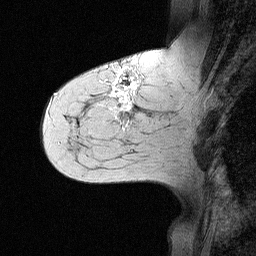
Breast MRI (dynamic contrast-enhanced), one sagittal slice; slice 21 of 64 in the series (ordered by position); dynamic contrast-enhanced study with each time point stored as its own series, time point 2 of 3 at this slice position (early post-contrast, ordered by acquisition time); 1.5 T; TE 4.5 ms, TR 11 ms; 256 × 256 image matrix. Female patient, age 55 years. From the clinical record (not read from this slice): setting: breast cancer imaged before/during neoadjuvant chemotherapy; receptor status: triple-negative.
Structures marked on this image (semi-automatically segmented with operator editing):
- analysis volume of interest (the breast-tissue region the enhancement analysis was run in; not a lesion): bounding box (x1, y1, x2, y2) in pixels: (71, 63, 147, 145)
- tumour enhancement mask (voxels above the 90 % enhancement threshold inside the analysis volume of interest): (105, 68, 141, 110)